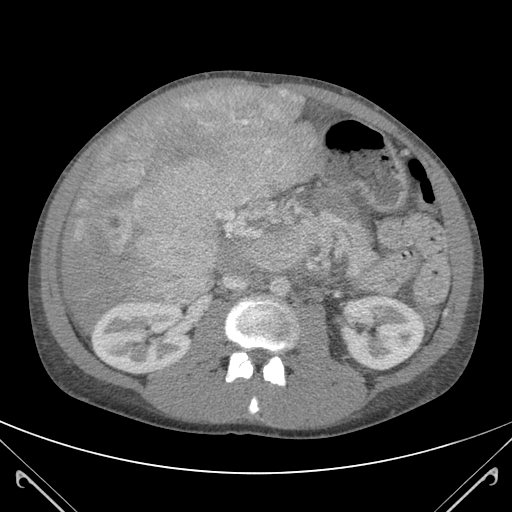
Contrast-enhanced abdominal CT (liver protocol), one axial slice. Position 55 of 118 along the scan axis. 120 kVp. Soft-tissue window (W 400 / L 40 HU). 3 mm slice thickness. 512 × 512 image matrix, field of view 380 × 380 mm. From the clinical record (not read from this slice): diagnosis: hepatocellular carcinoma (patient treated with transarterial chemoembolisation; whether this scan precedes or follows treatment is not stated here); TNM stage (as recorded): Stage-IIIB; Child-Pugh class: A.
Structures marked on this image (semi-automatically segmented with operator editing):
- abdominal aorta: box from (x=270, y=278) to (x=290, y=298) px
- liver parenchyma outside the tumour (the mass and vessels are separate outlines, so this box may not span the whole liver): (x=59, y=85)–(x=322, y=326)
- mass: (x=69, y=86)–(x=320, y=305)
- liver vessels: (x=184, y=103)–(x=291, y=237)